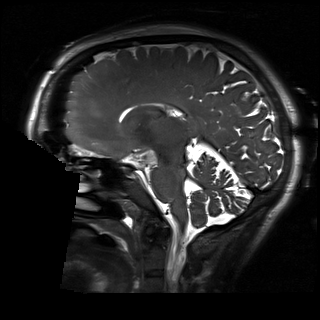
Brain MRI from a brain-tumour surgery series, one sagittal slice. Slice 104 of 192 in the series (ordered by position). 320 × 320 image matrix, field of view 230 × 230 mm. From the clinical record (not read from this slice): histopathology: Glioblastoma; WHO grade: 2; IDH mutation: no; tumour location: Right Skull Base Temporal.
Structures marked on this image (expert manual segmentation):
- residual tumour: box from (x=147, y=154) to (x=156, y=162) px